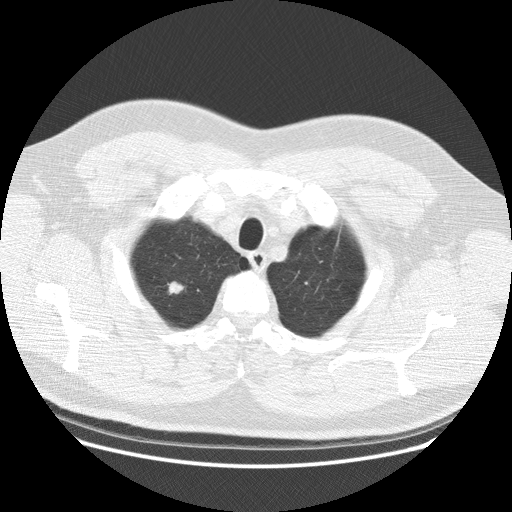
Low-dose screening chest CT, one axial slice. Slice 98 of 111 in the series (ordered by position). 120 kVp. Lung window (W 1500 / L -600 HU). 512 × 512 image matrix, field of view 389 × 389 mm.
Annotated regions visible in this slice (manually delineated by an expert):
- lesion 1 (tumor, upper lobe of right lung): bounding box <168,281,184,295> (left, top, right, bottom; pixels)